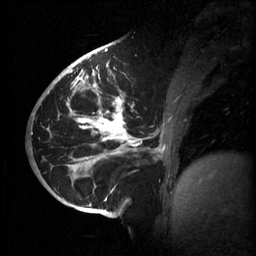
Breast MRI (dynamic contrast-enhanced), one sagittal slice; position 26 of 60 along the scan axis; 3 images stored at this slice position (order not interpretable as contrast timing); 1.5 T; TE 4.2 ms, TR 11 ms; 2 mm slice thickness; 256 × 256 image matrix, field of view 220 × 220 mm. Female patient, age 51 years.
Annotated regions visible in this slice (semi-automatically segmented with operator editing):
- analysis volume of interest (the breast-tissue region the enhancement analysis was run in; not a lesion): bounding box [x1, y1, x2, y2] px = [63, 80, 187, 201]
- tumour enhancement mask (voxels above the 70 % enhancement threshold inside the analysis volume of interest): [67, 80, 166, 201]